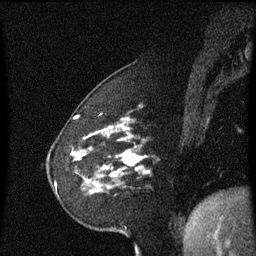
Breast MRI (dynamic contrast-enhanced), one sagittal slice. Slice 15 of 60 in the series (ordered by position). Dynamic contrast-enhanced series, image 2 of 3 at this slice position (ordered by acquisition). 1.5 T. TE 4.2 ms, TR 8.4 ms. 256 × 256 image matrix, field of view 200 × 200 mm. Patient: female, 60 years. Case-level facts recorded for this patient, not image findings: setting: breast cancer imaged before/during neoadjuvant chemotherapy; receptor status: triple-negative.
Outlined on this slice (semi-automatic segmentation, software-assisted and operator-edited):
- analysis volume of interest (the breast-tissue region the enhancement analysis was run in; not a lesion): bounding box [x1, y1, x2, y2] px = [71, 148, 141, 195]
- tumour enhancement mask (voxels above the 70 % enhancement threshold inside the analysis volume of interest): [111, 152, 140, 177]